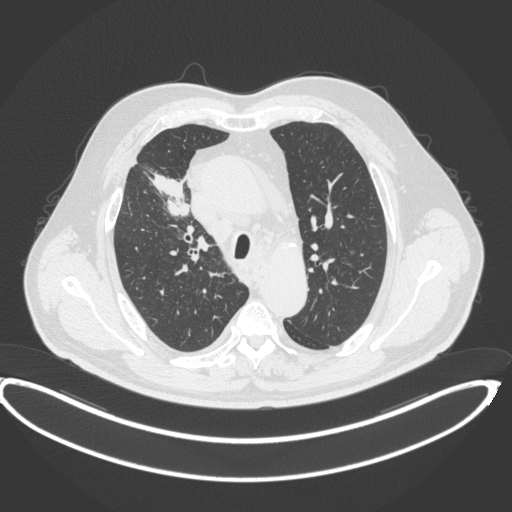
Chest CT, one axial slice; slice 291 of 395 in the series (ordered by position); 120 kVp; lung window (W 1500 / L -600 HU); 1 mm slice thickness; 512 × 512 image matrix, field of view 448 × 448 mm. Patient: male, 62 years. From the clinical record (not read from this slice): clinical TNM (as recorded): T1c N3 M1c.
Structures marked on this image (rectangle marked by the reading radiologist):
- lung tumour (recorded histology: adenocarcinoma): box from (x=144, y=167) to (x=190, y=218) px